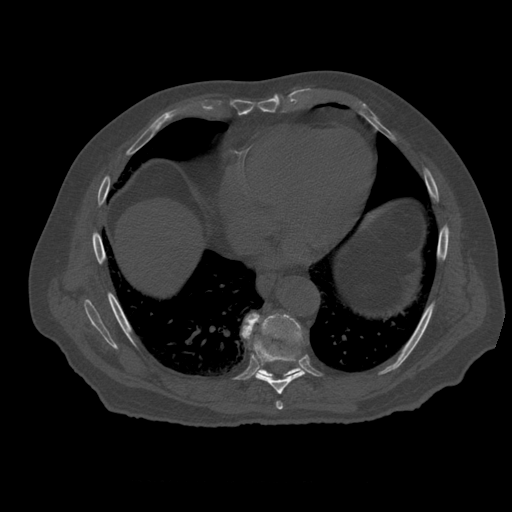
CT including the spine, one axial slice. Position 334 of 399 along the scan axis. Reconstruction kernel STANDARD. Bone window (W 1800 / L 400 HU). 1.25 mm slice thickness. 512 × 512 image matrix. Patient age 73 years. Case-level facts recorded for this patient, not image findings: primary cancer: prostate; vertebrae with lytic lesions (as recorded): L2.
Annotated regions visible in this slice (semi-automatically segmented with operator editing):
- T7 vertebra: bounding box [x1, y1, x2, y2] px = [276, 402, 284, 410]
- T8 vertebra: [251, 339, 305, 395]
- T9 vertebra: [243, 313, 303, 378]